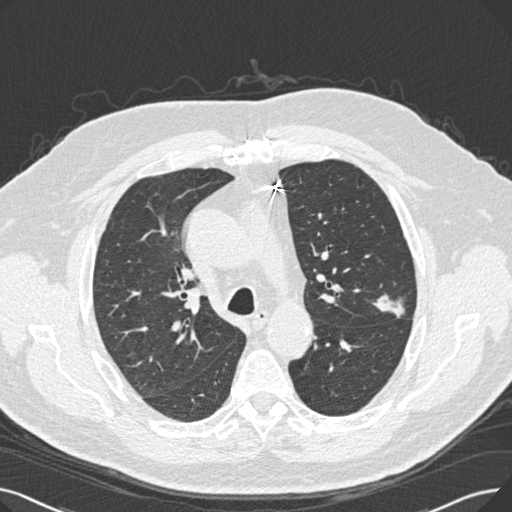
Low-dose screening chest CT, one axial slice. Slice 178 of 269 in the series (ordered by position). Reconstruction kernel B30f. 120 kVp. Lung window (W 1500 / L -600 HU). 512 × 512 image matrix.
Structures marked on this image (manually delineated by an expert):
- lesion 1 (tumor, upper lobe of left lung): box from (x=372, y=294) to (x=405, y=318) px